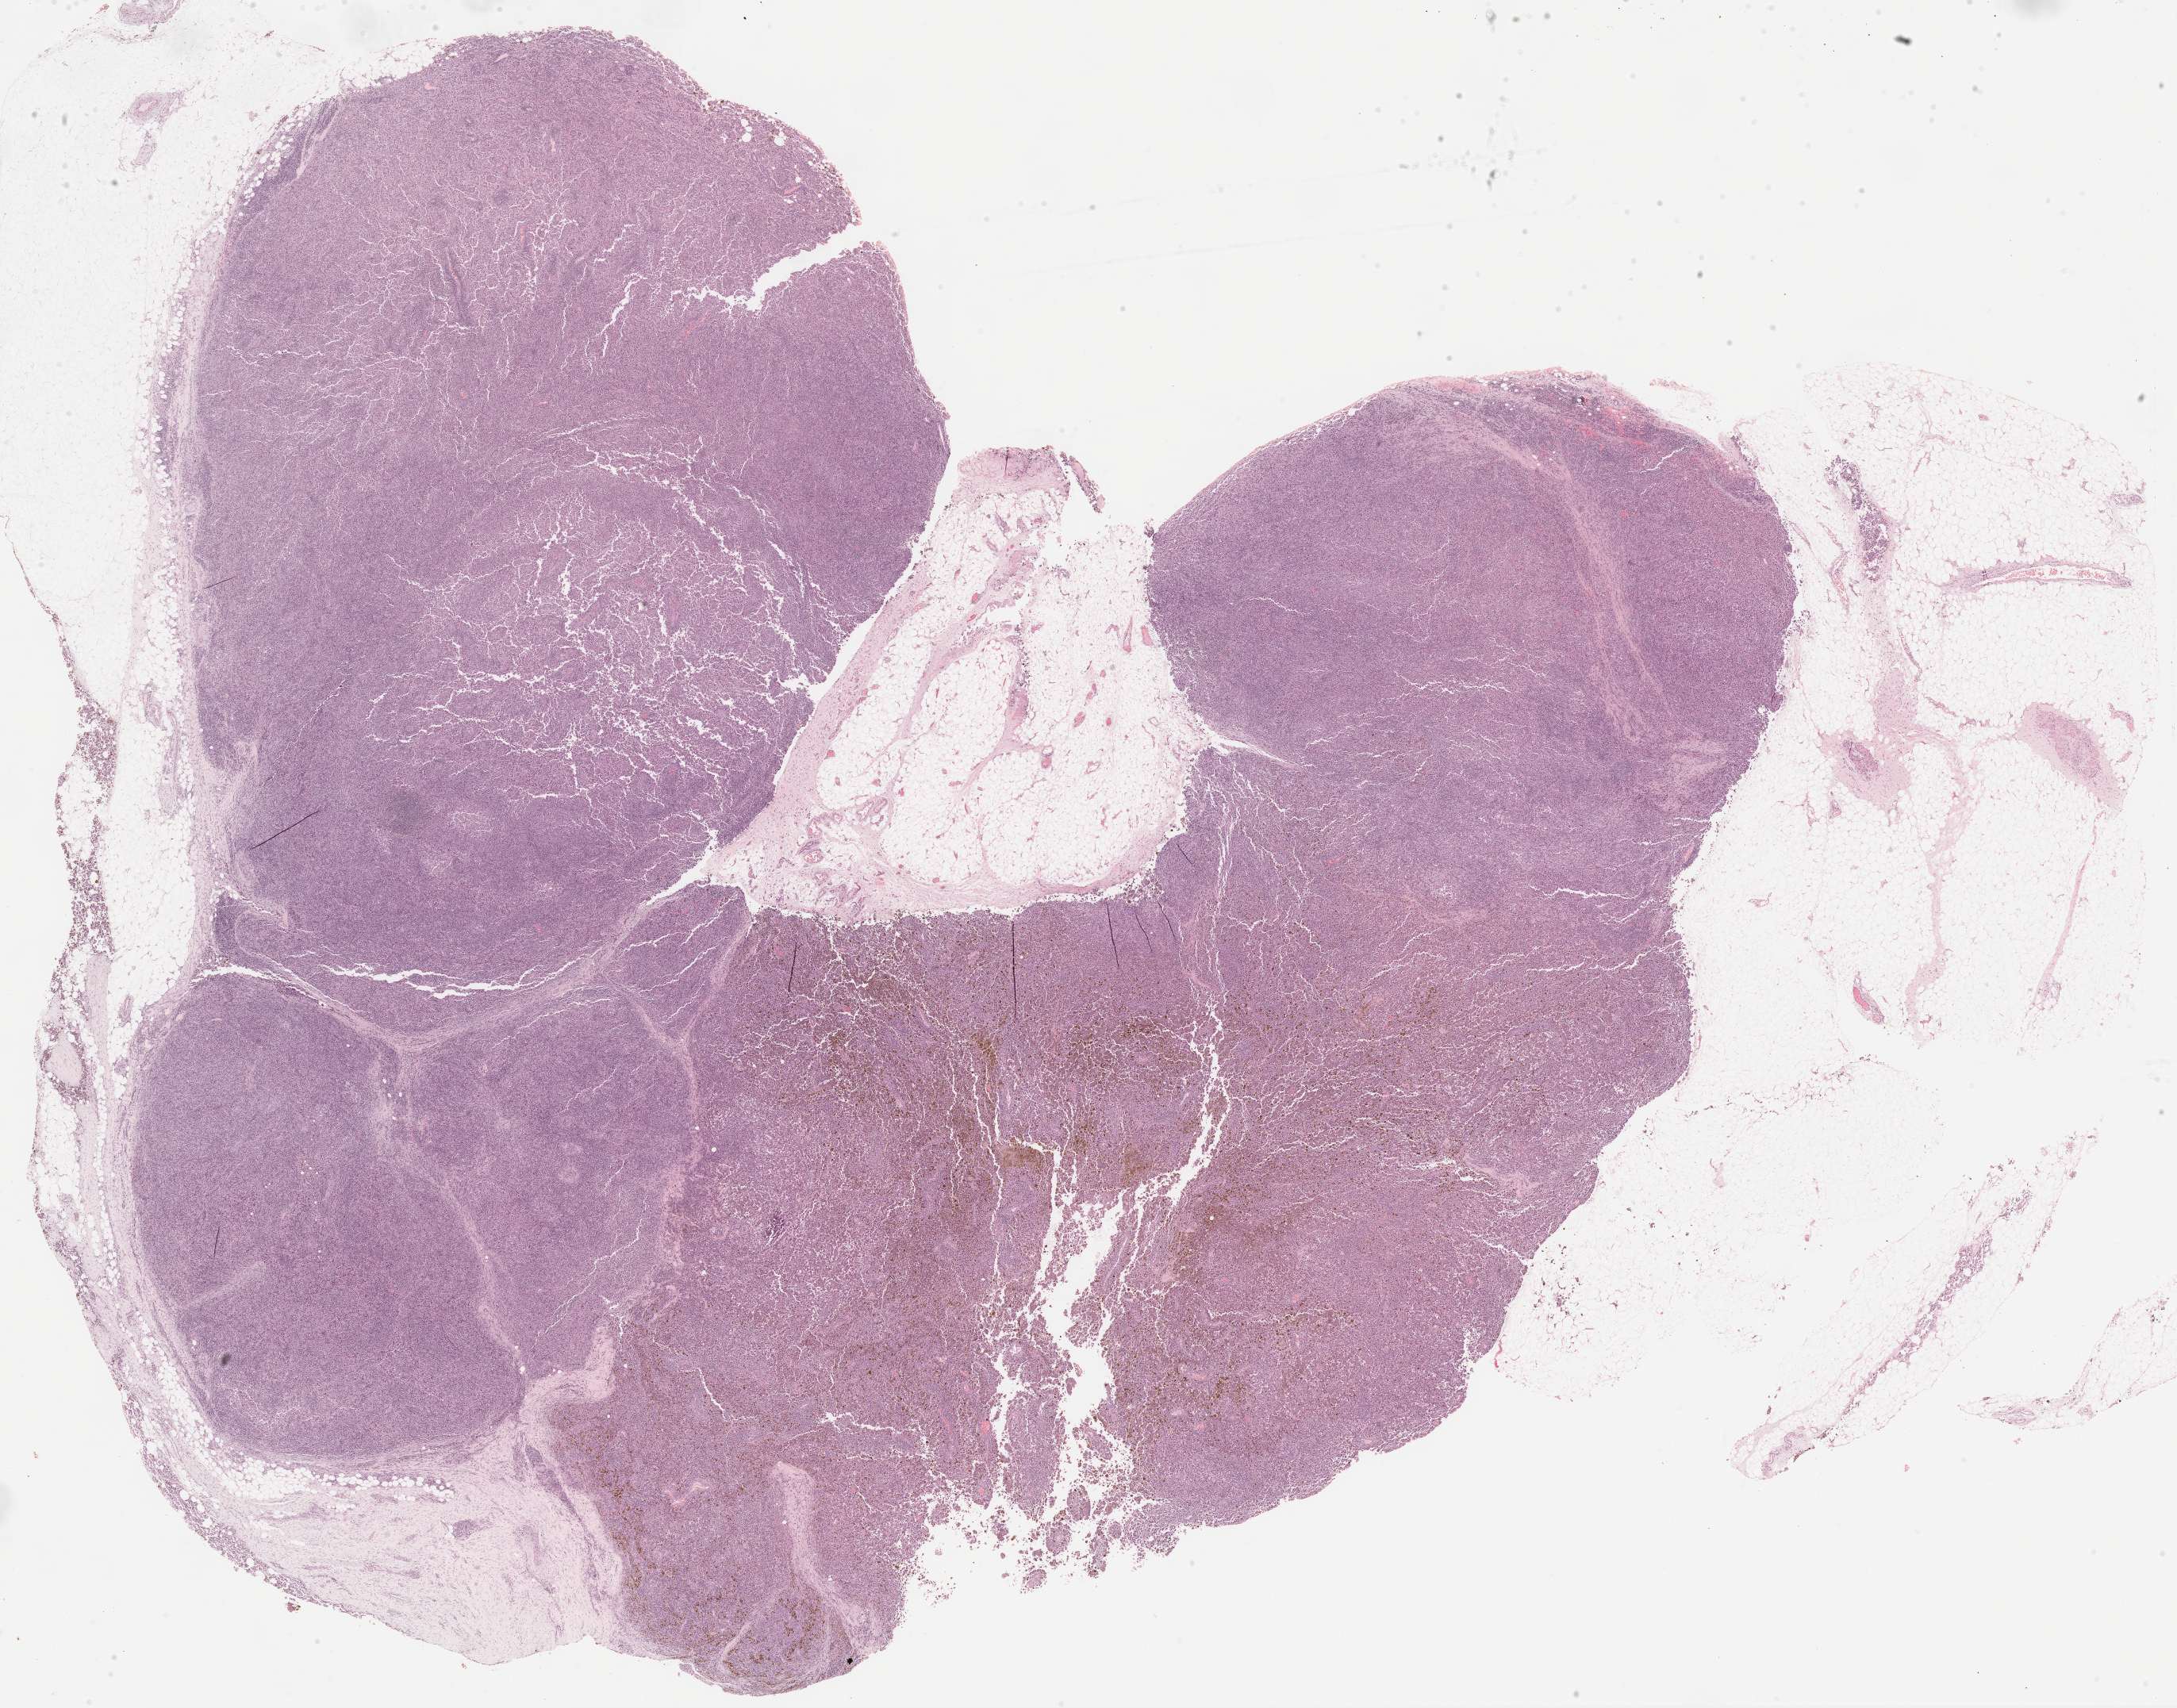
H&E whole-slide image — a low-resolution overview of the entire scanned area, about 22.1 x 17.4 mm. Formalin-fixed paraffin-embedded (FFPE) diagnostic section. Metastatic tumour sample. Female, age 42 years at initial diagnosis.
* this section: metastatic tumour tissue
* patient diagnosis: Malignant melanoma, NOS